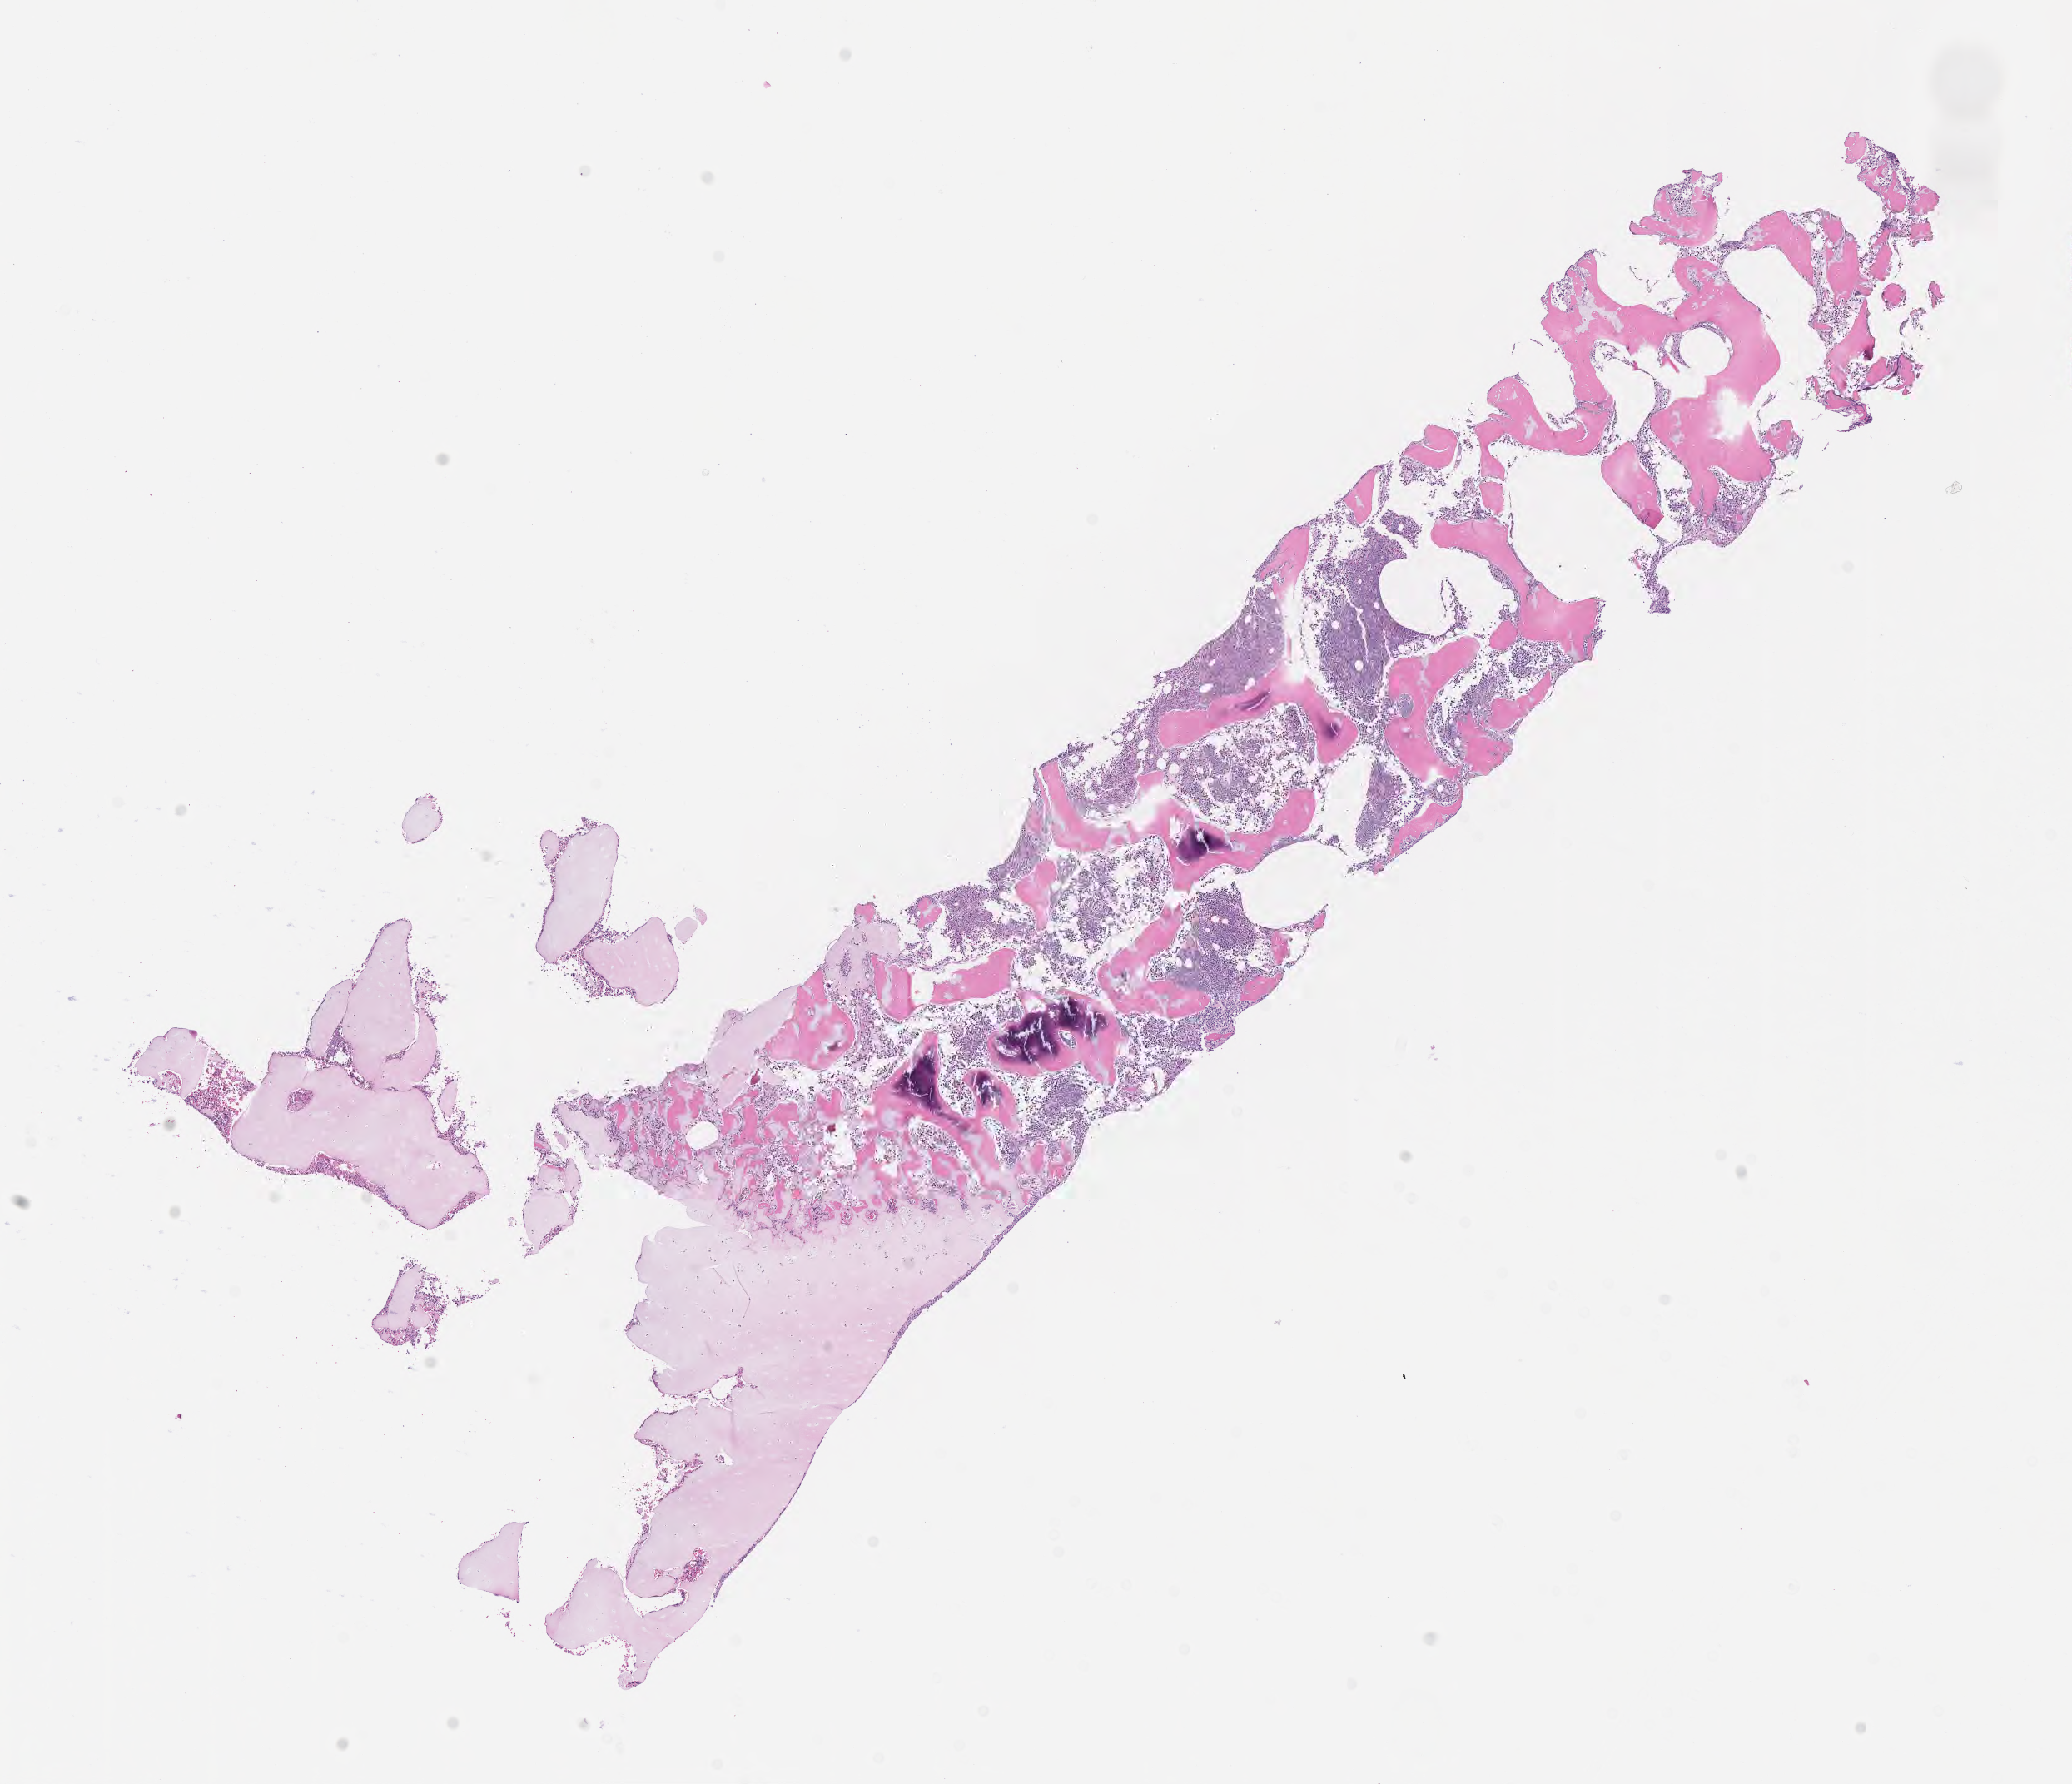
Haematoxylin and eosin whole-slide image — a low-resolution overview of the entire scanned area, about 10.1 x 8.7 mm, specimen: tumor tissue. Patient: male, 13 years old.
Diagnosis: Burkitt lymphoma, NOS.